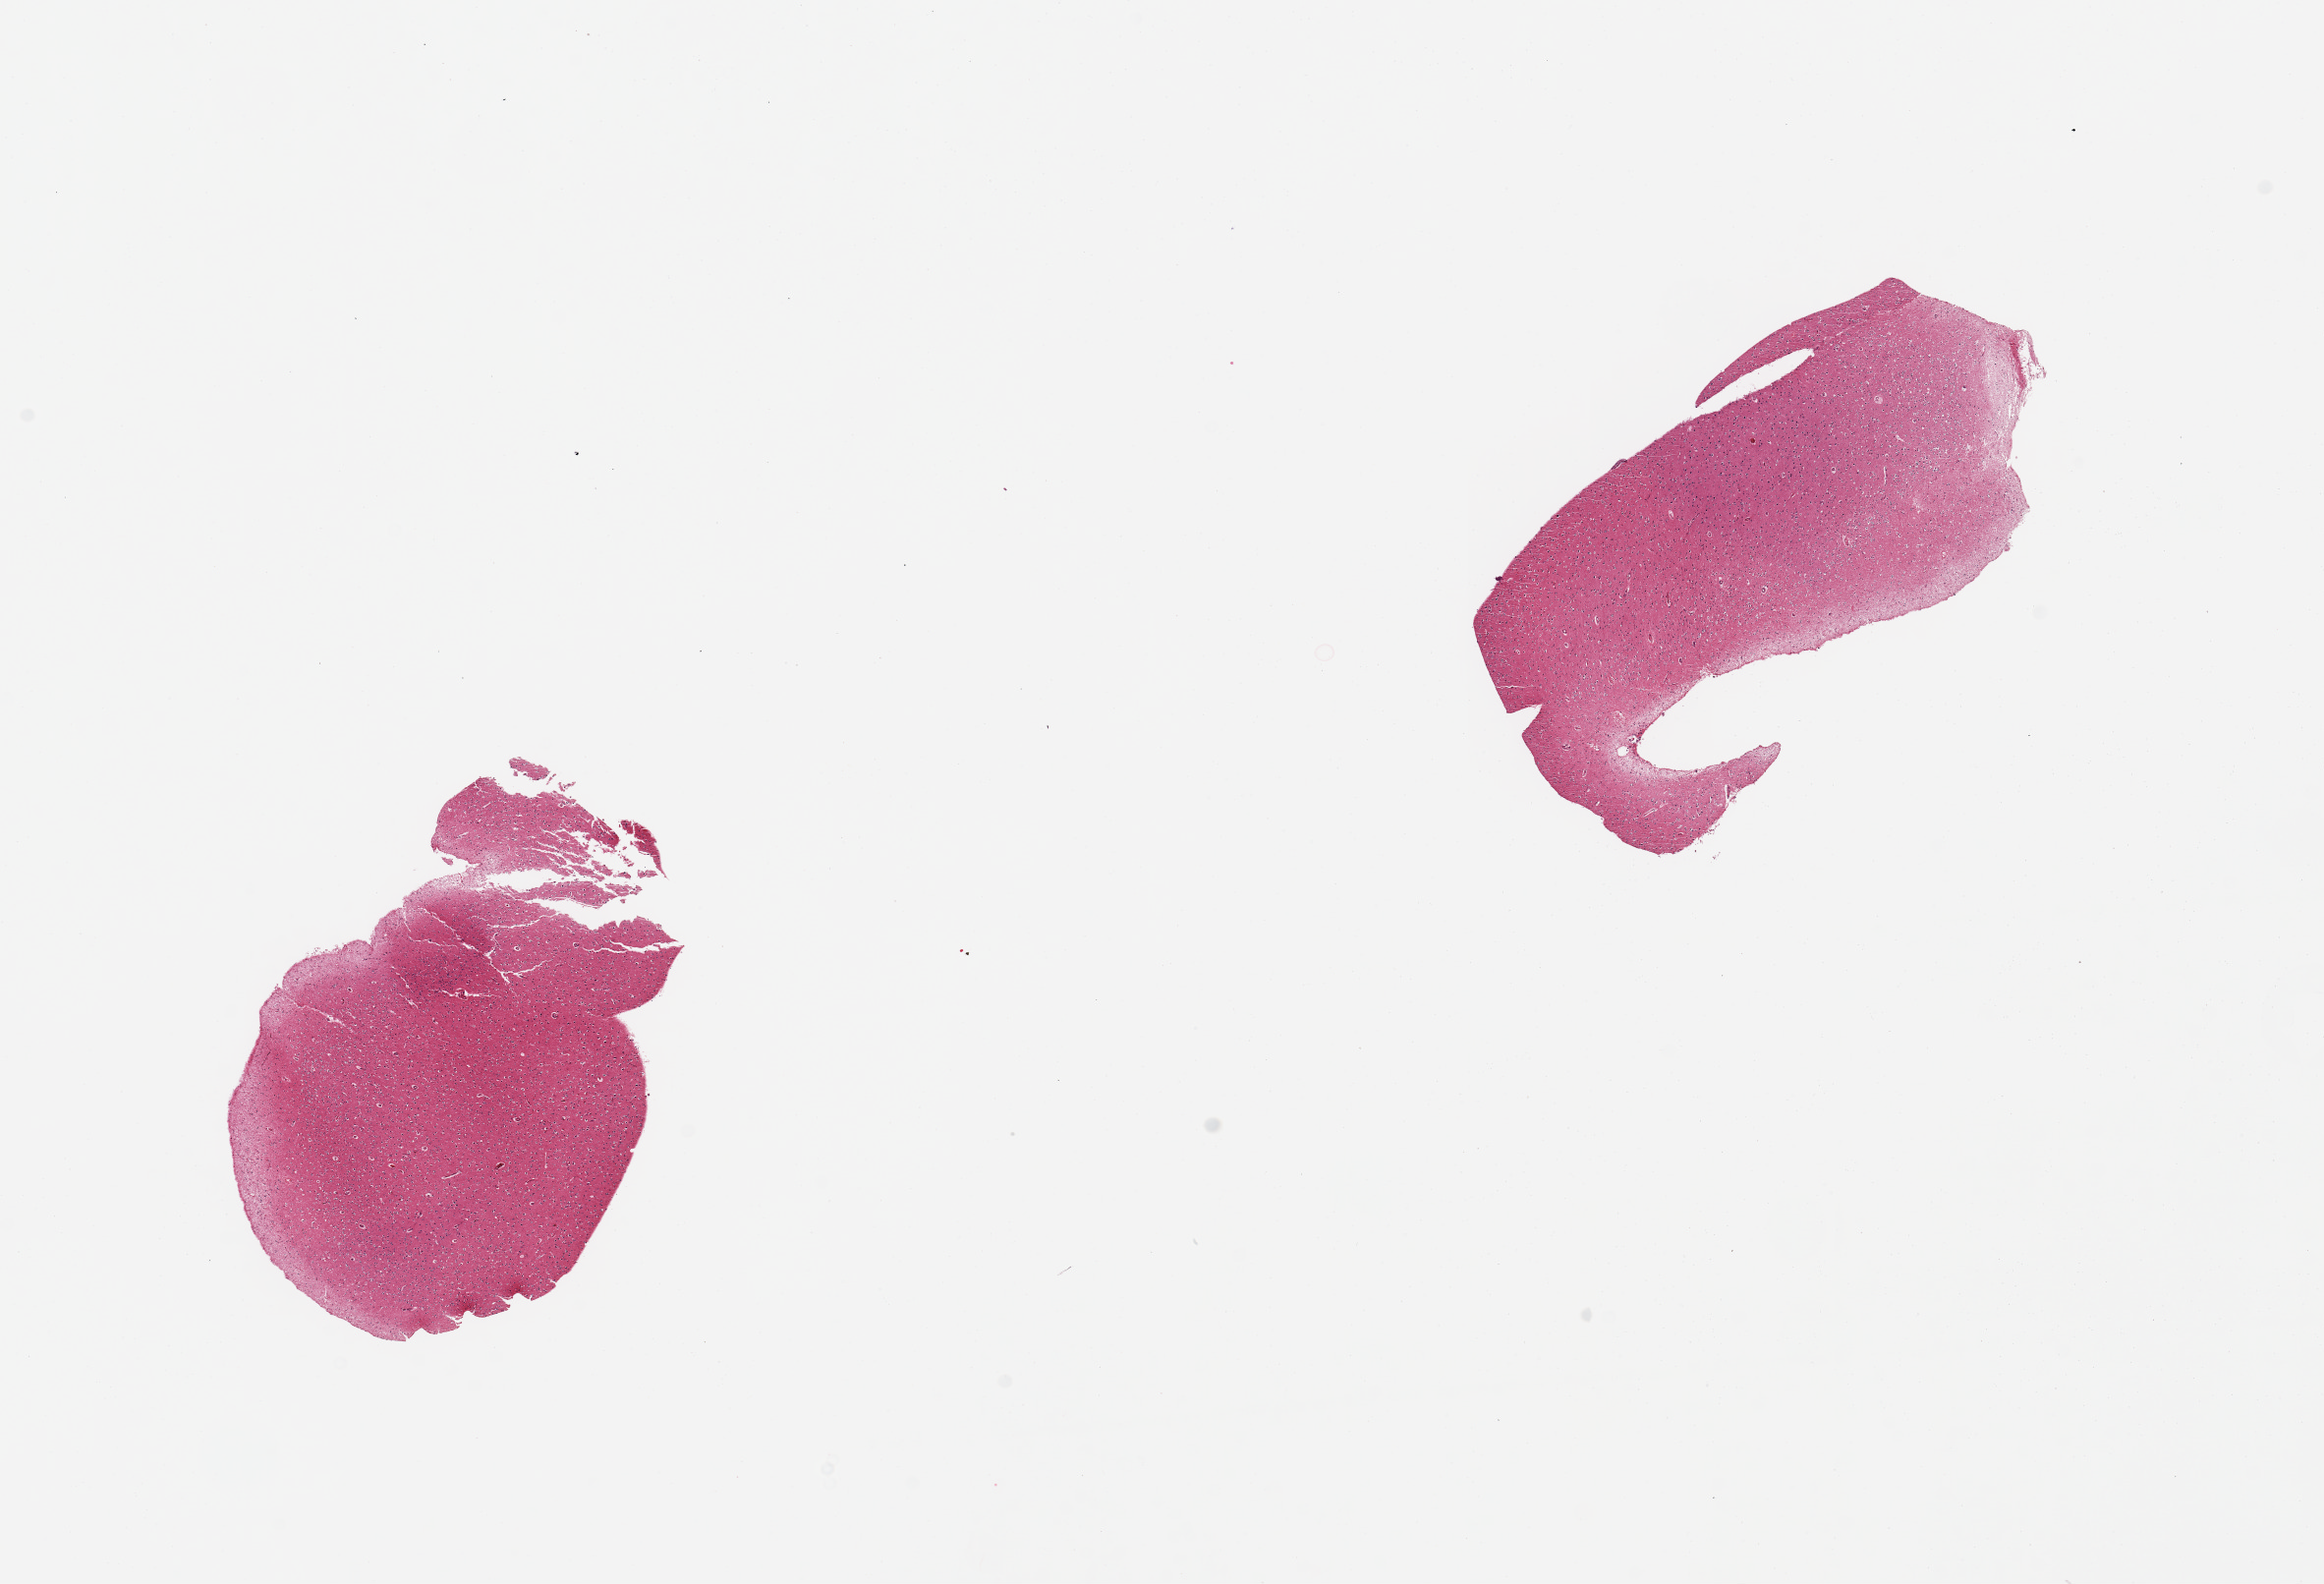
Digitized haematoxylin and eosin-stained section, brightfield, whole scanned area (about 18.7 x 12.7 mm) shown as a low-resolution overview. PAXgene-fixed paraffin-embedded (PFPE) section. Section of cerebral cortex (target tissue). Donor tissue sample.
* pathologist's review note for this sample: 2 pieces